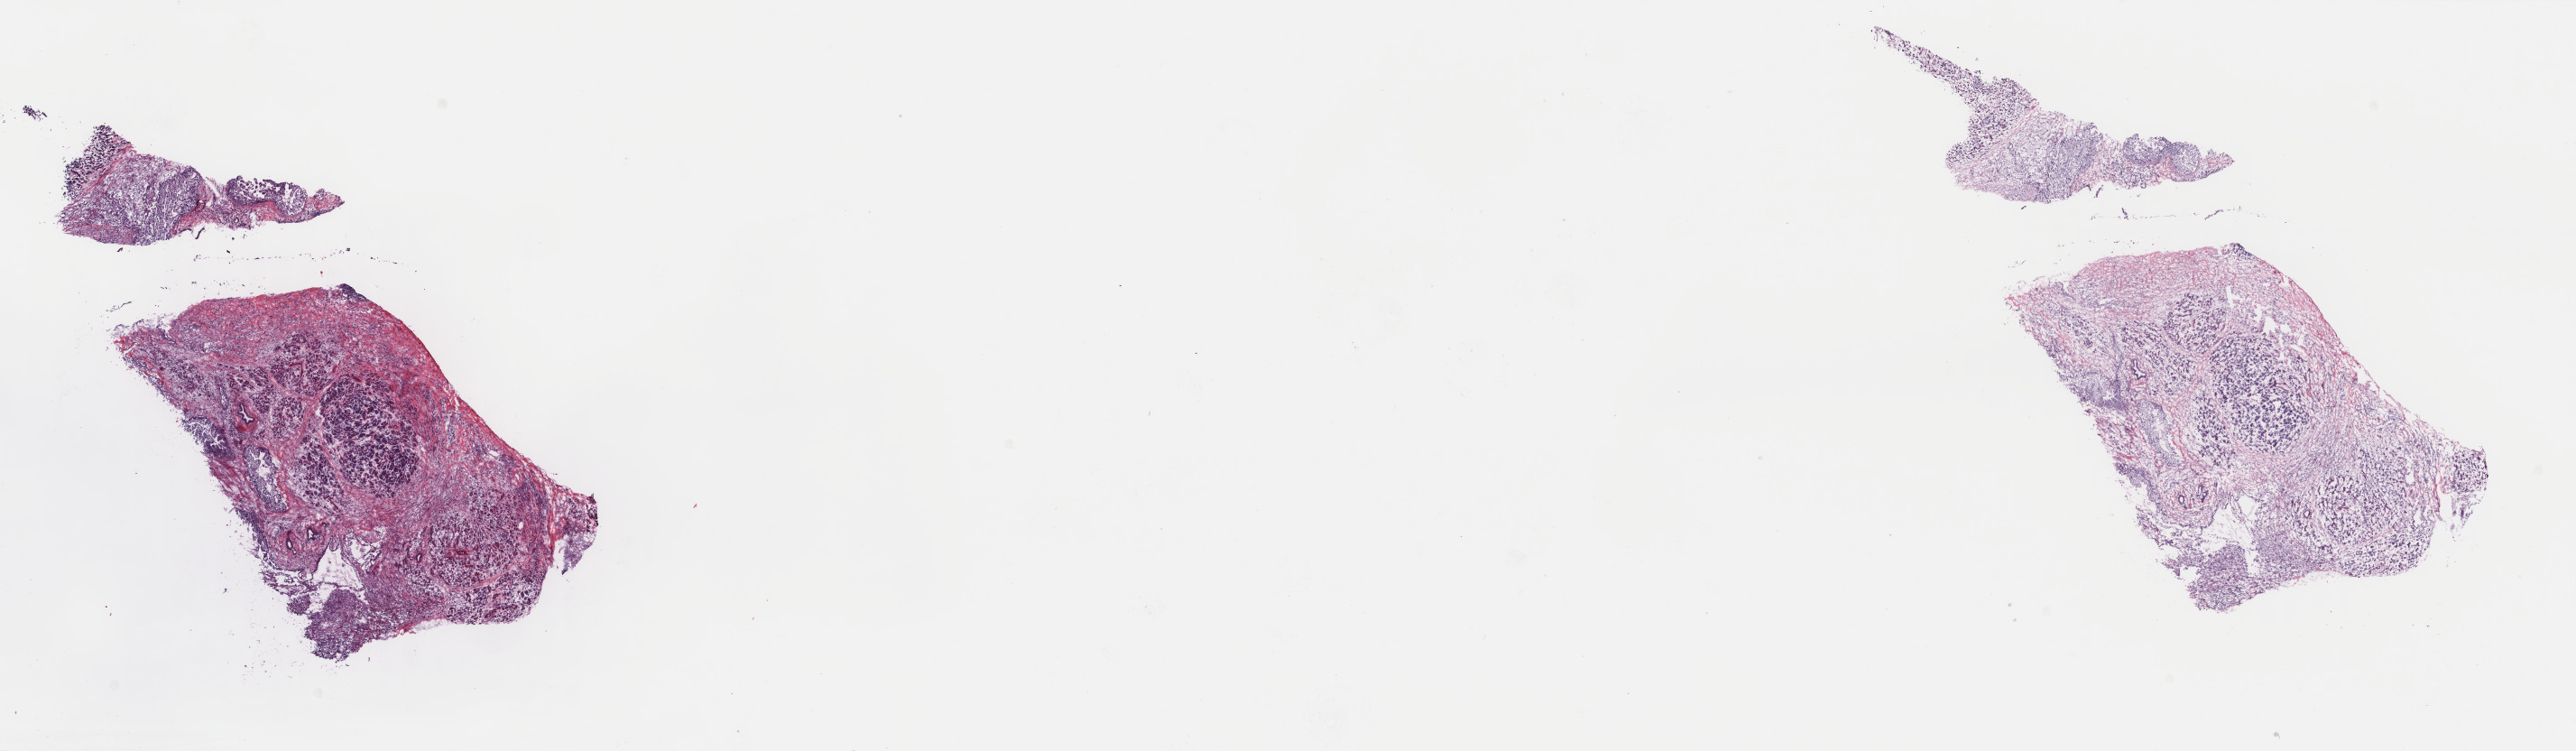
H&E-stained whole-slide image, shown as a low-resolution overview of the whole scanned area (about 22.7 x 6.6 mm). Frozen section. Pancreas, primary tumour sample. Patient: female, age at initial diagnosis 76 years. Histologic grade: G3 (poorly differentiated). Pathologist review of this section (percent, as recorded): tumour cells 50%, tumour nuclei 60%, normal cells 0%, stromal cells 50%, necrosis 0%. Inflammatory infiltration, as recorded: lymphocyte infiltration 0%, monocyte infiltration 0%, neutrophil infiltration 0%.
Histologic diagnosis: Infiltrating duct carcinoma, NOS (head of pancreas). AJCC pathologic stage: IIB. Lymph nodes positive (case pathology): 2 of 17 examined.